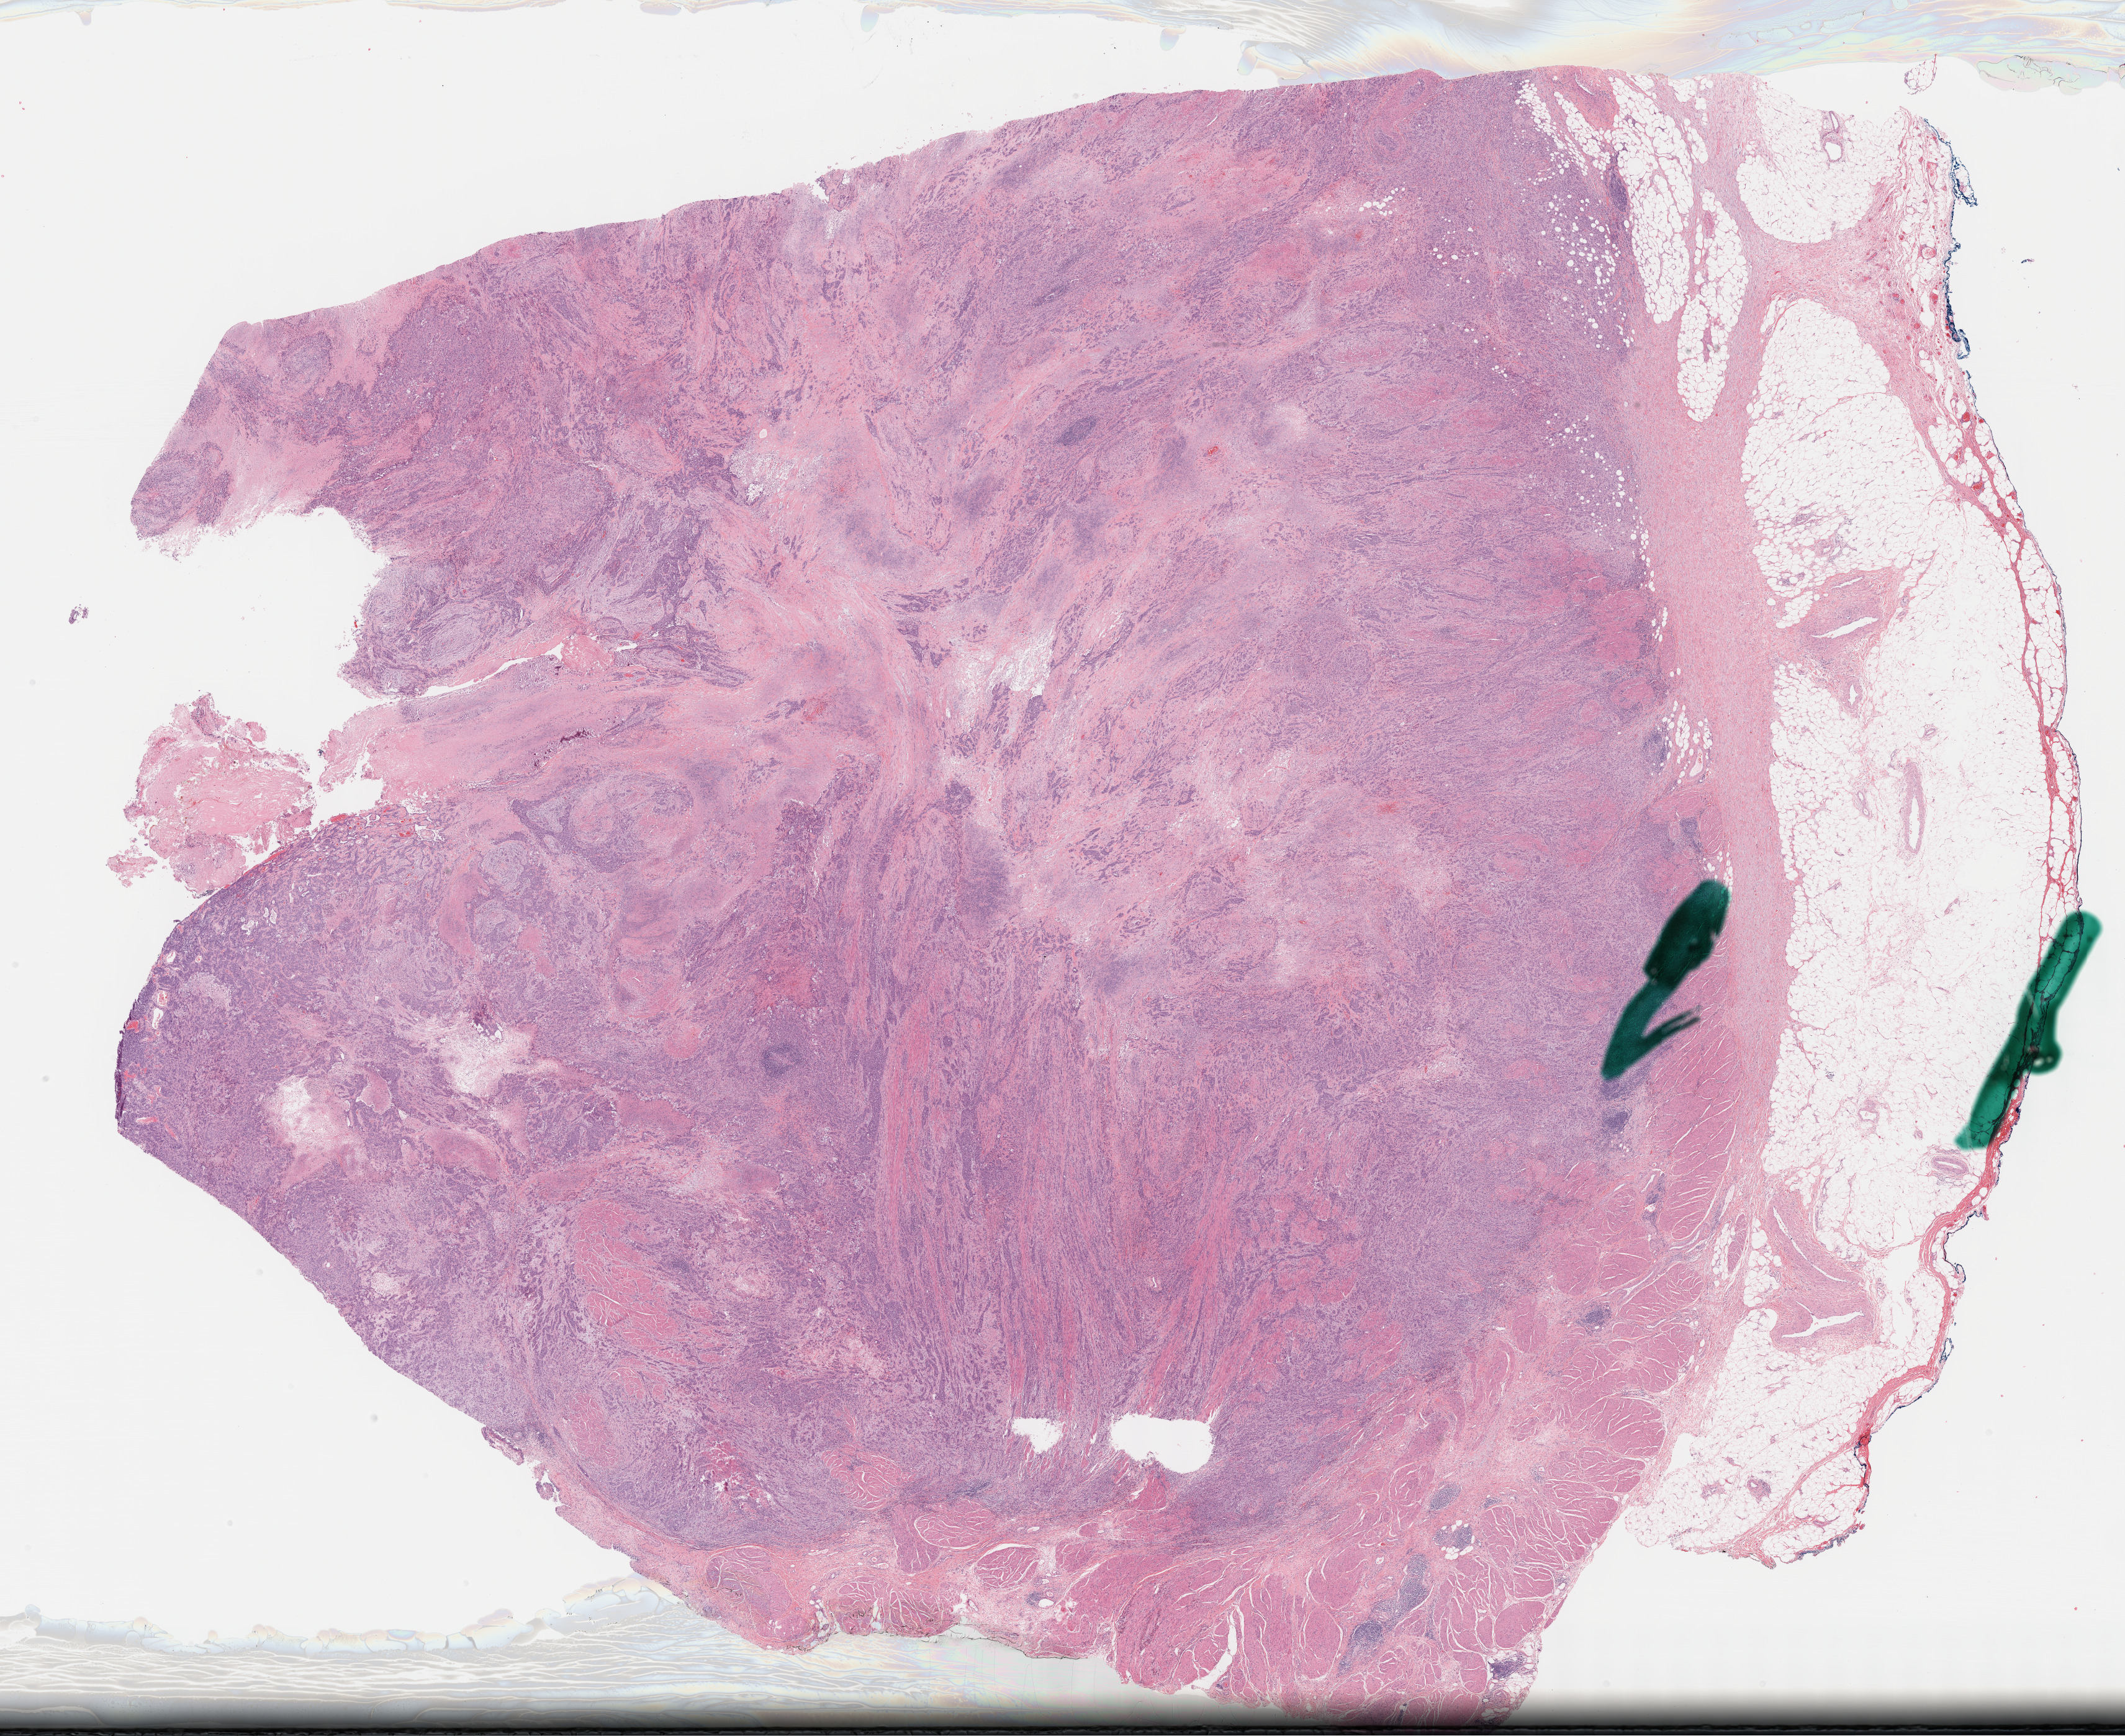
H&E whole-slide image — low-resolution overview of the scanned area, about 27.7 x 22.6 mm (slide scanned at 40x), FFPE section, primary tumour sample from the bladder. Patient: male, age at initial diagnosis 47 years. Histologic grade: high grade.
AJCC pathologic stage: III (6th edition). Histologic diagnosis: Transitional cell carcinoma (lateral wall of bladder).